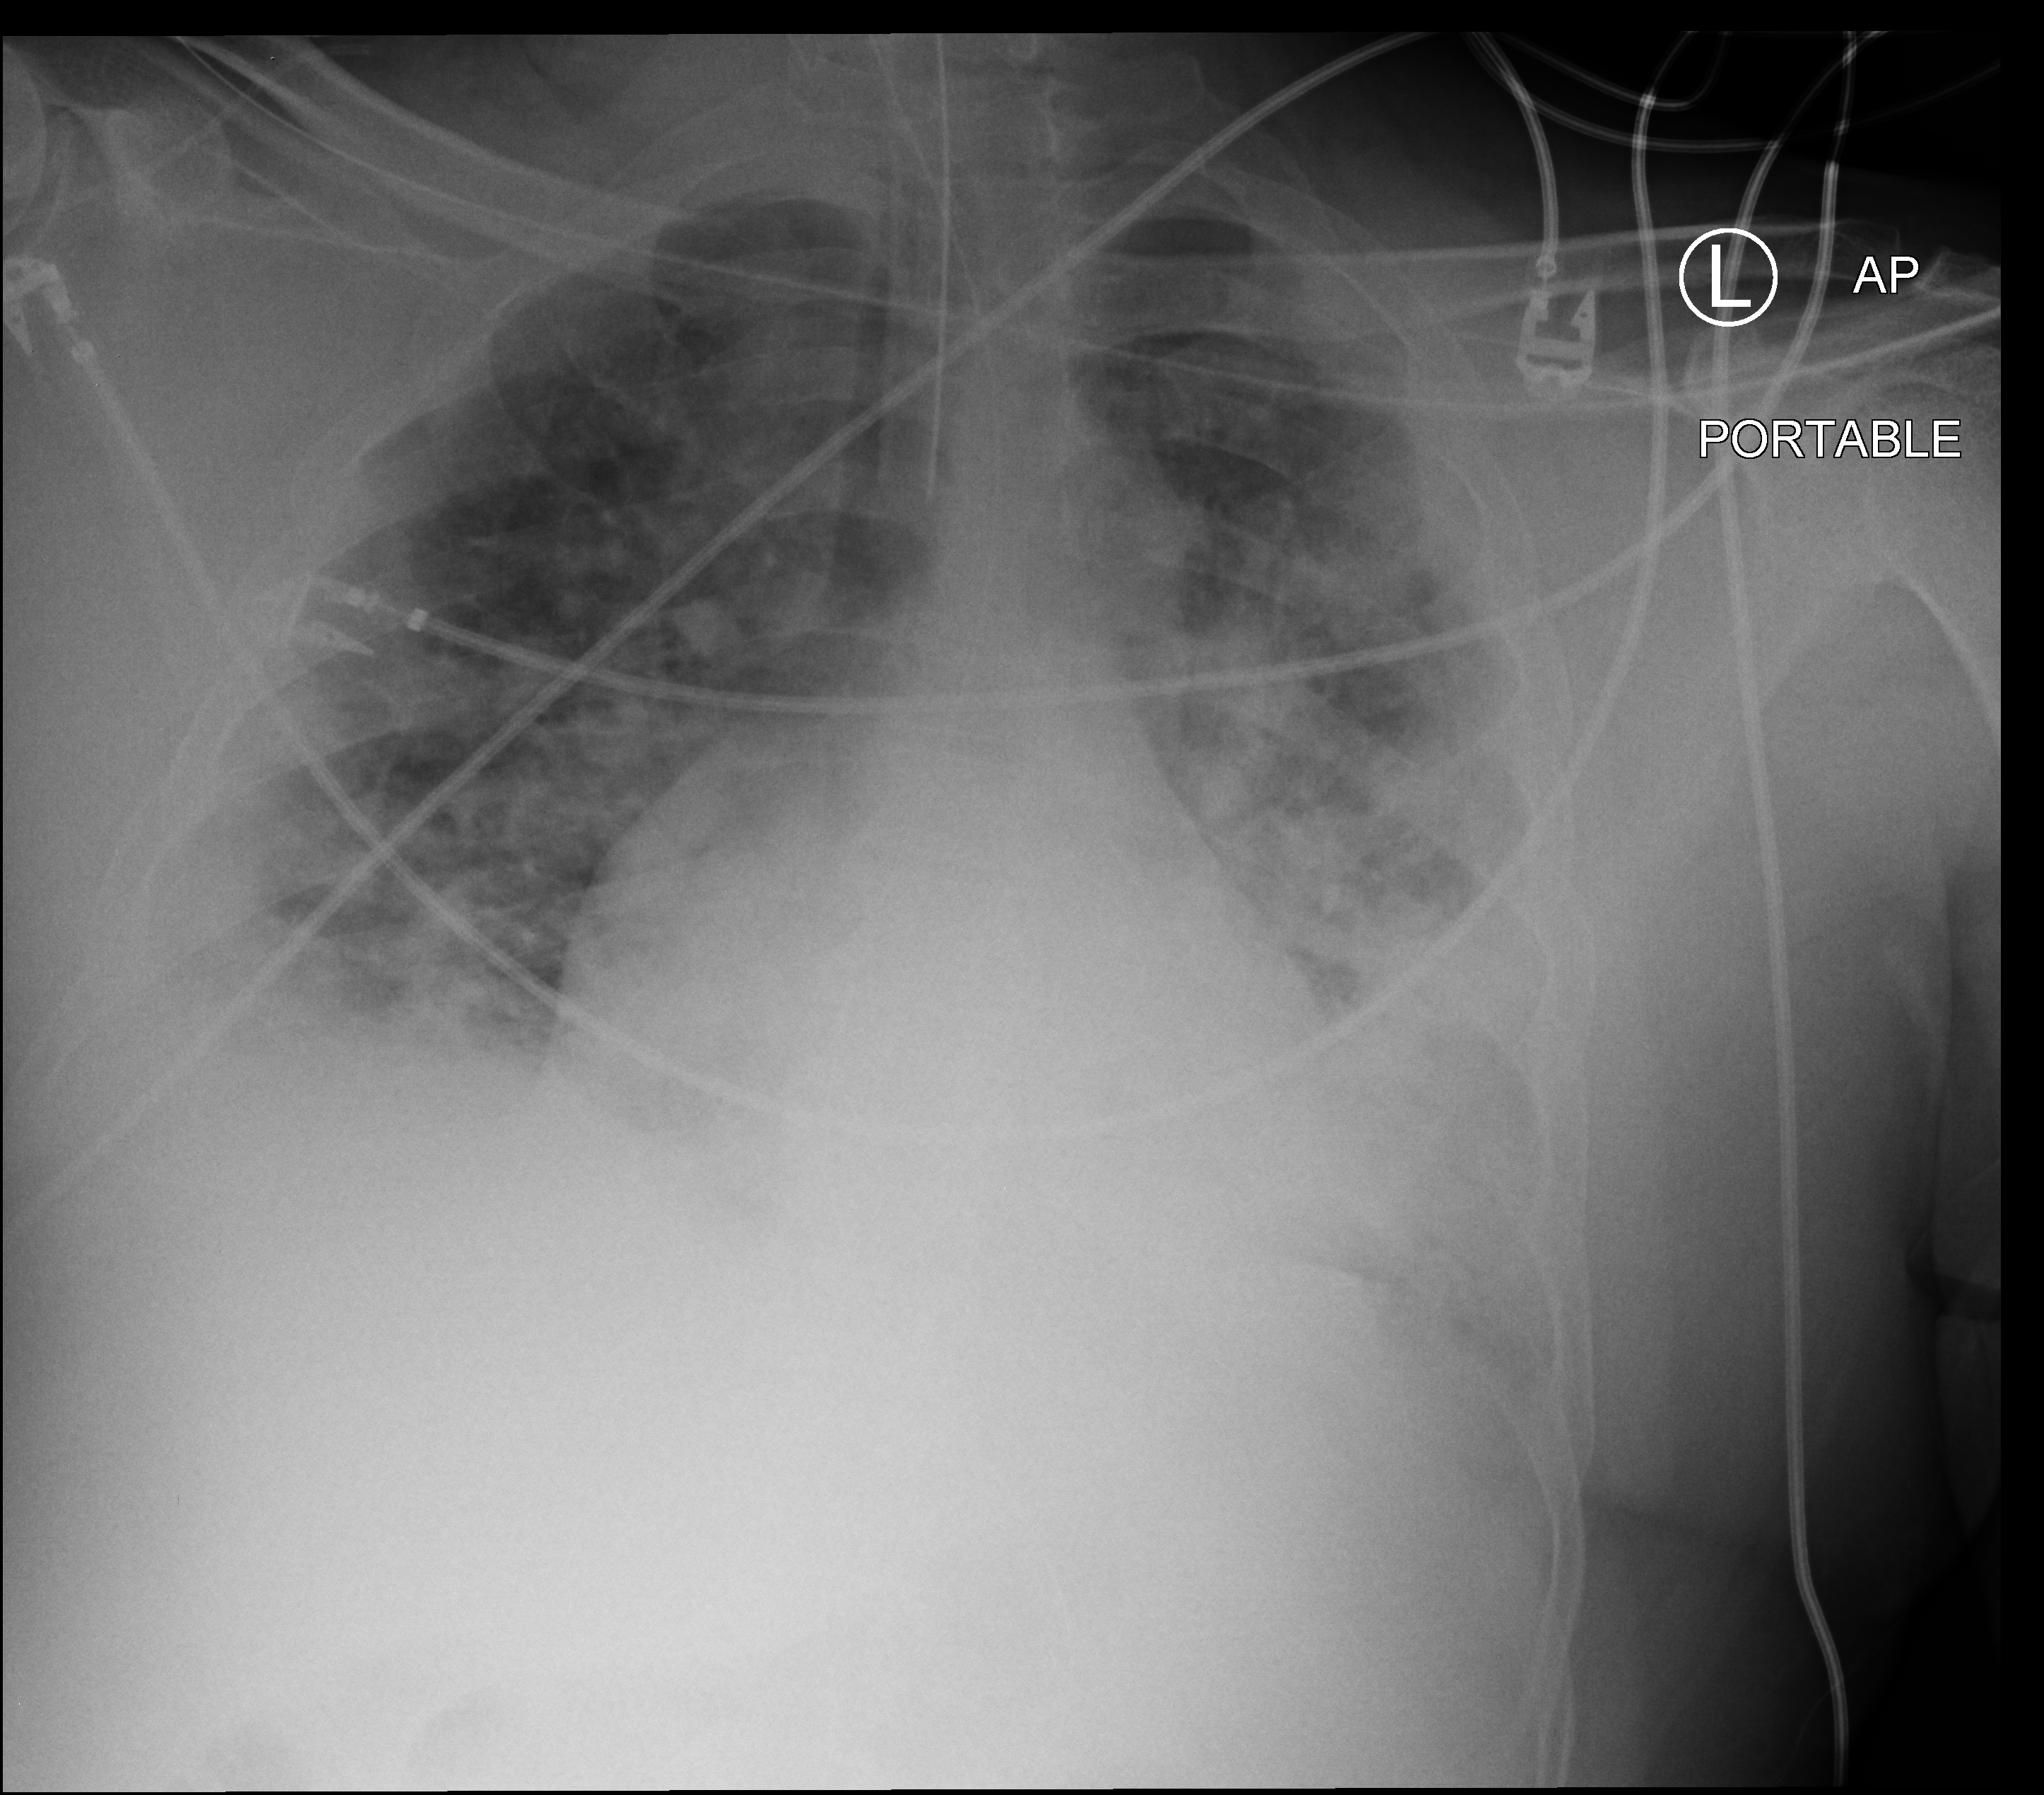
Chest X-ray (portable). Male patient hospitalised with COVID-19, age 18–59 years.
Hospital-stay facts (about this admission, not read from this image; timing relative to this image not recorded): chronic kidney disease (admission record): no; admitted to intensive care during this hospital stay: yes; mechanically ventilated during this hospital stay: yes.